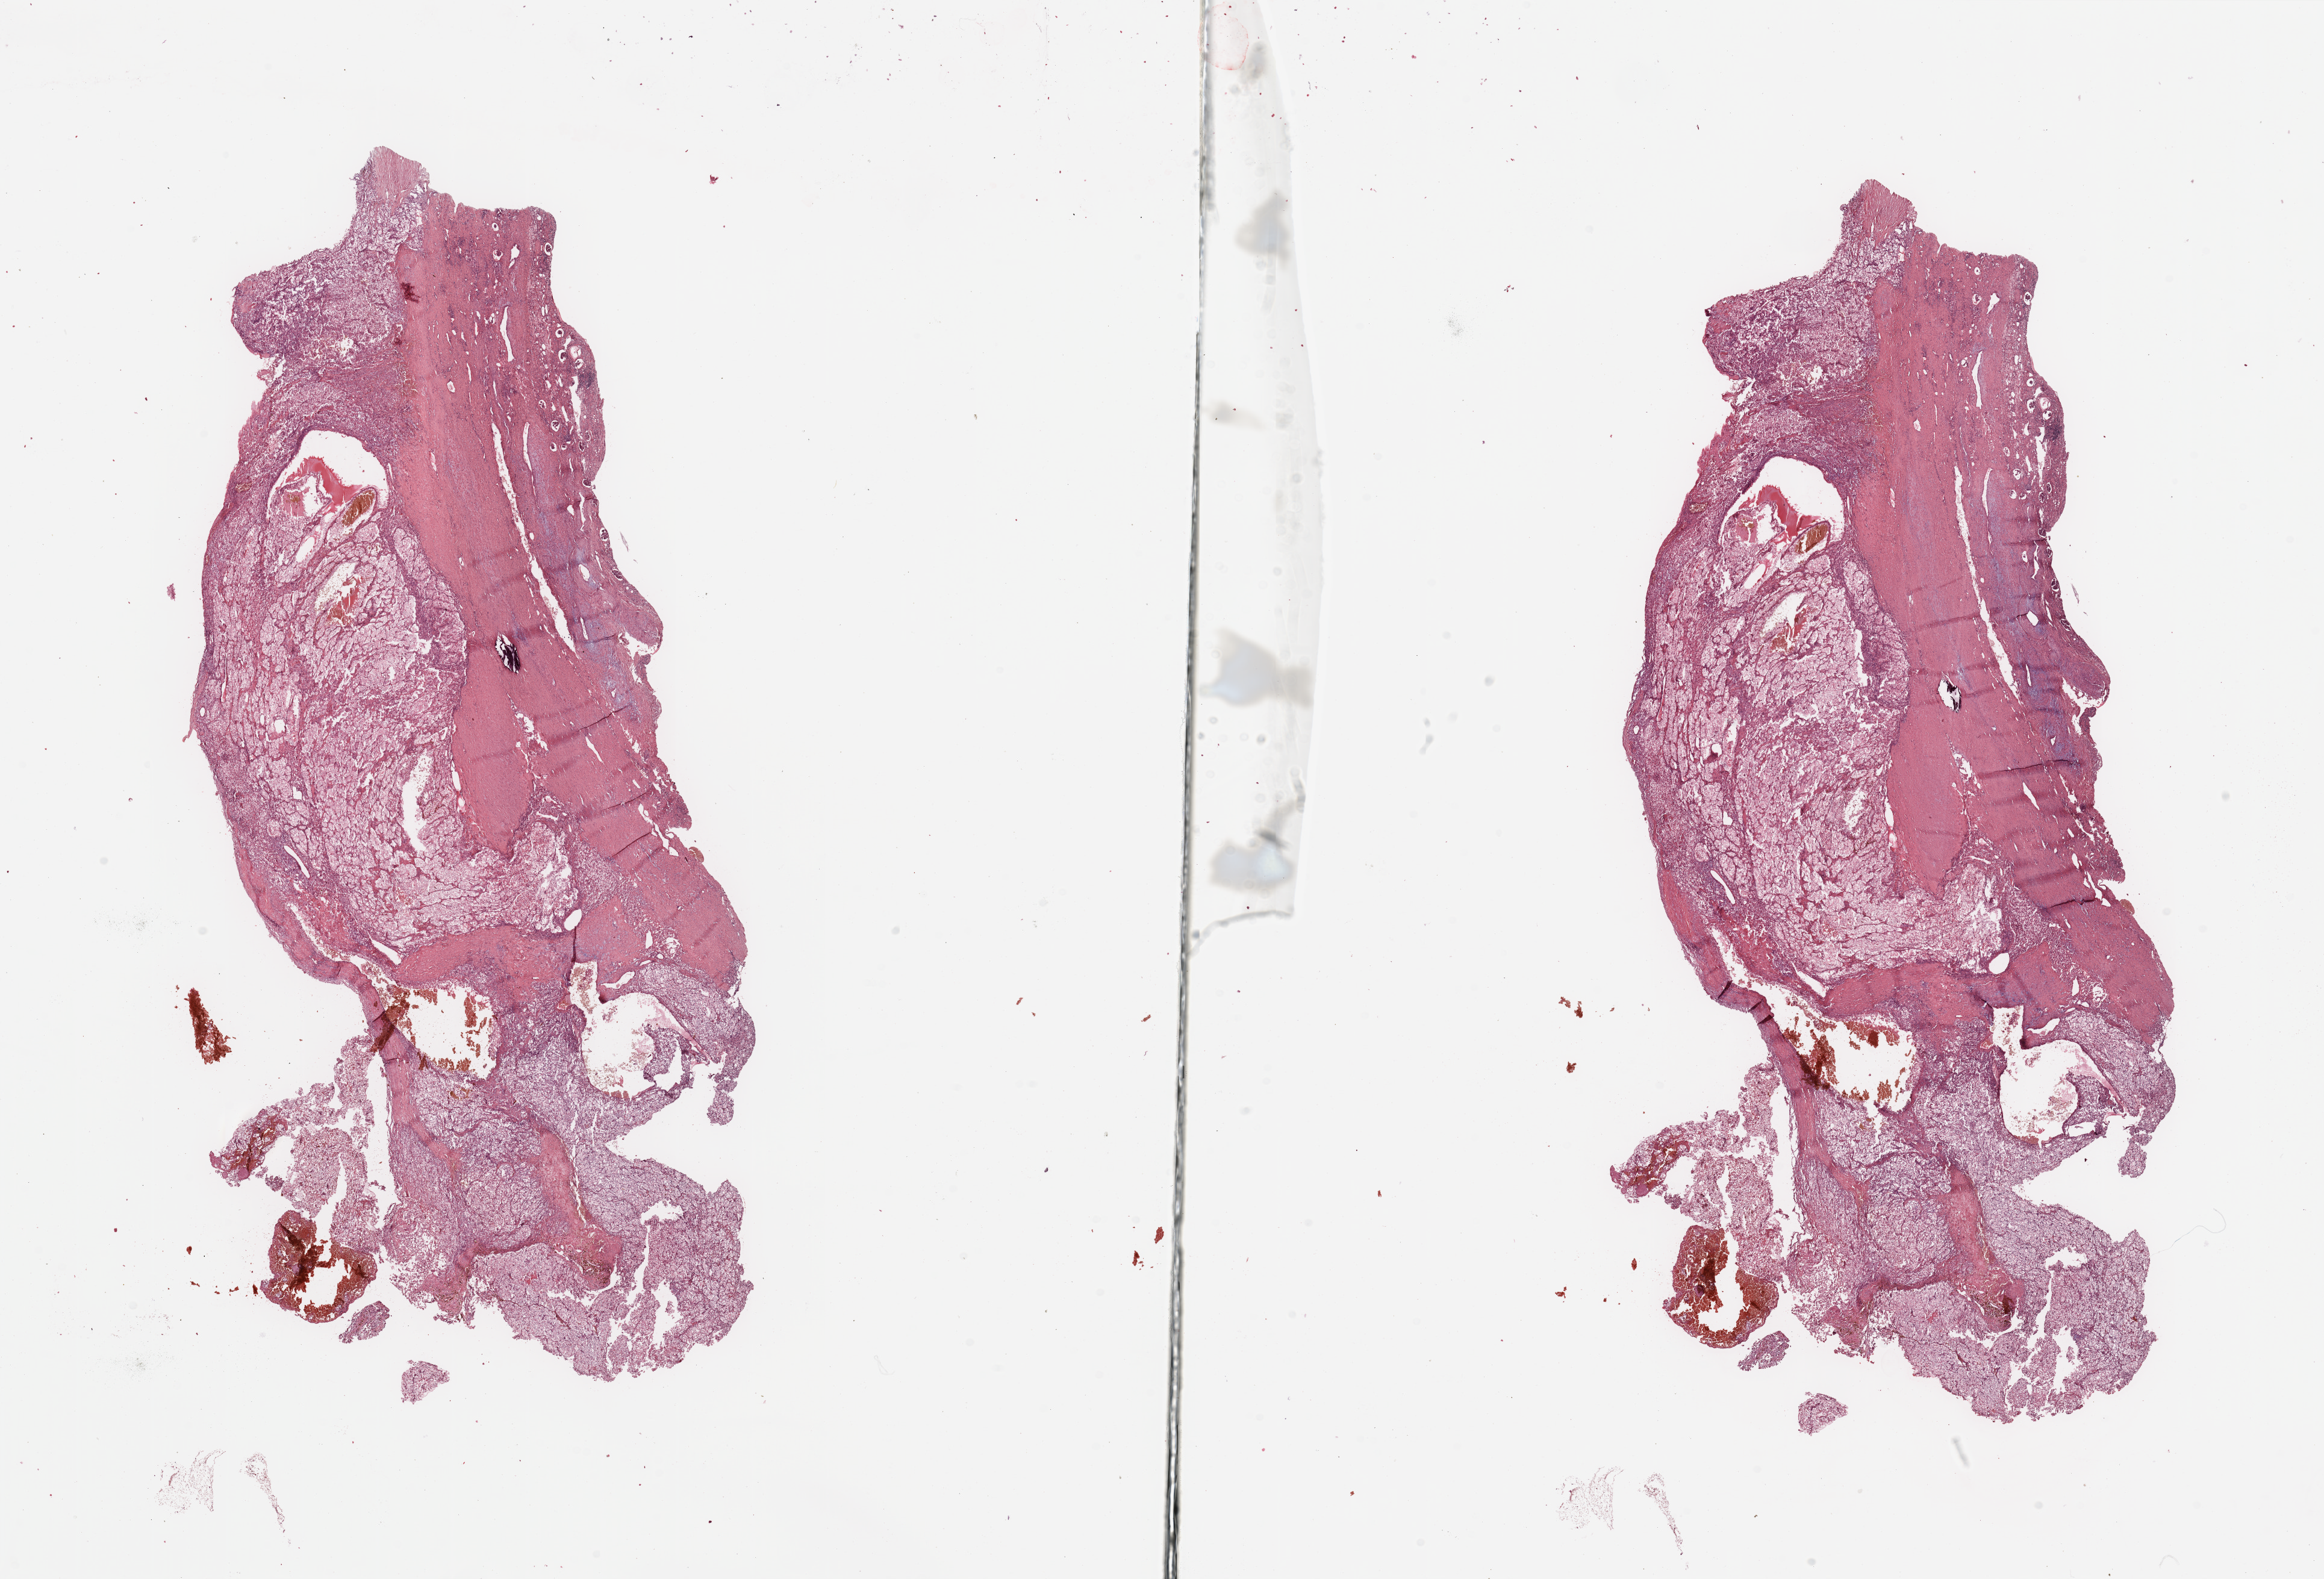
Whole-slide histology image, Hematoxylin and eosin (H&E) stained, low-resolution overview of the scanned area, about 30.5 x 20.7 mm; tumour tissue sample, sampled site: kidney. Patient: male, age 58 years. Histologic grade: G2 (moderately differentiated). Composition of this section per pathologist review: tumour nuclei 80%, necrosis 2%.
- histologic diagnosis: Renal cell carcinoma, NOS
- AJCC pathologic stage: III